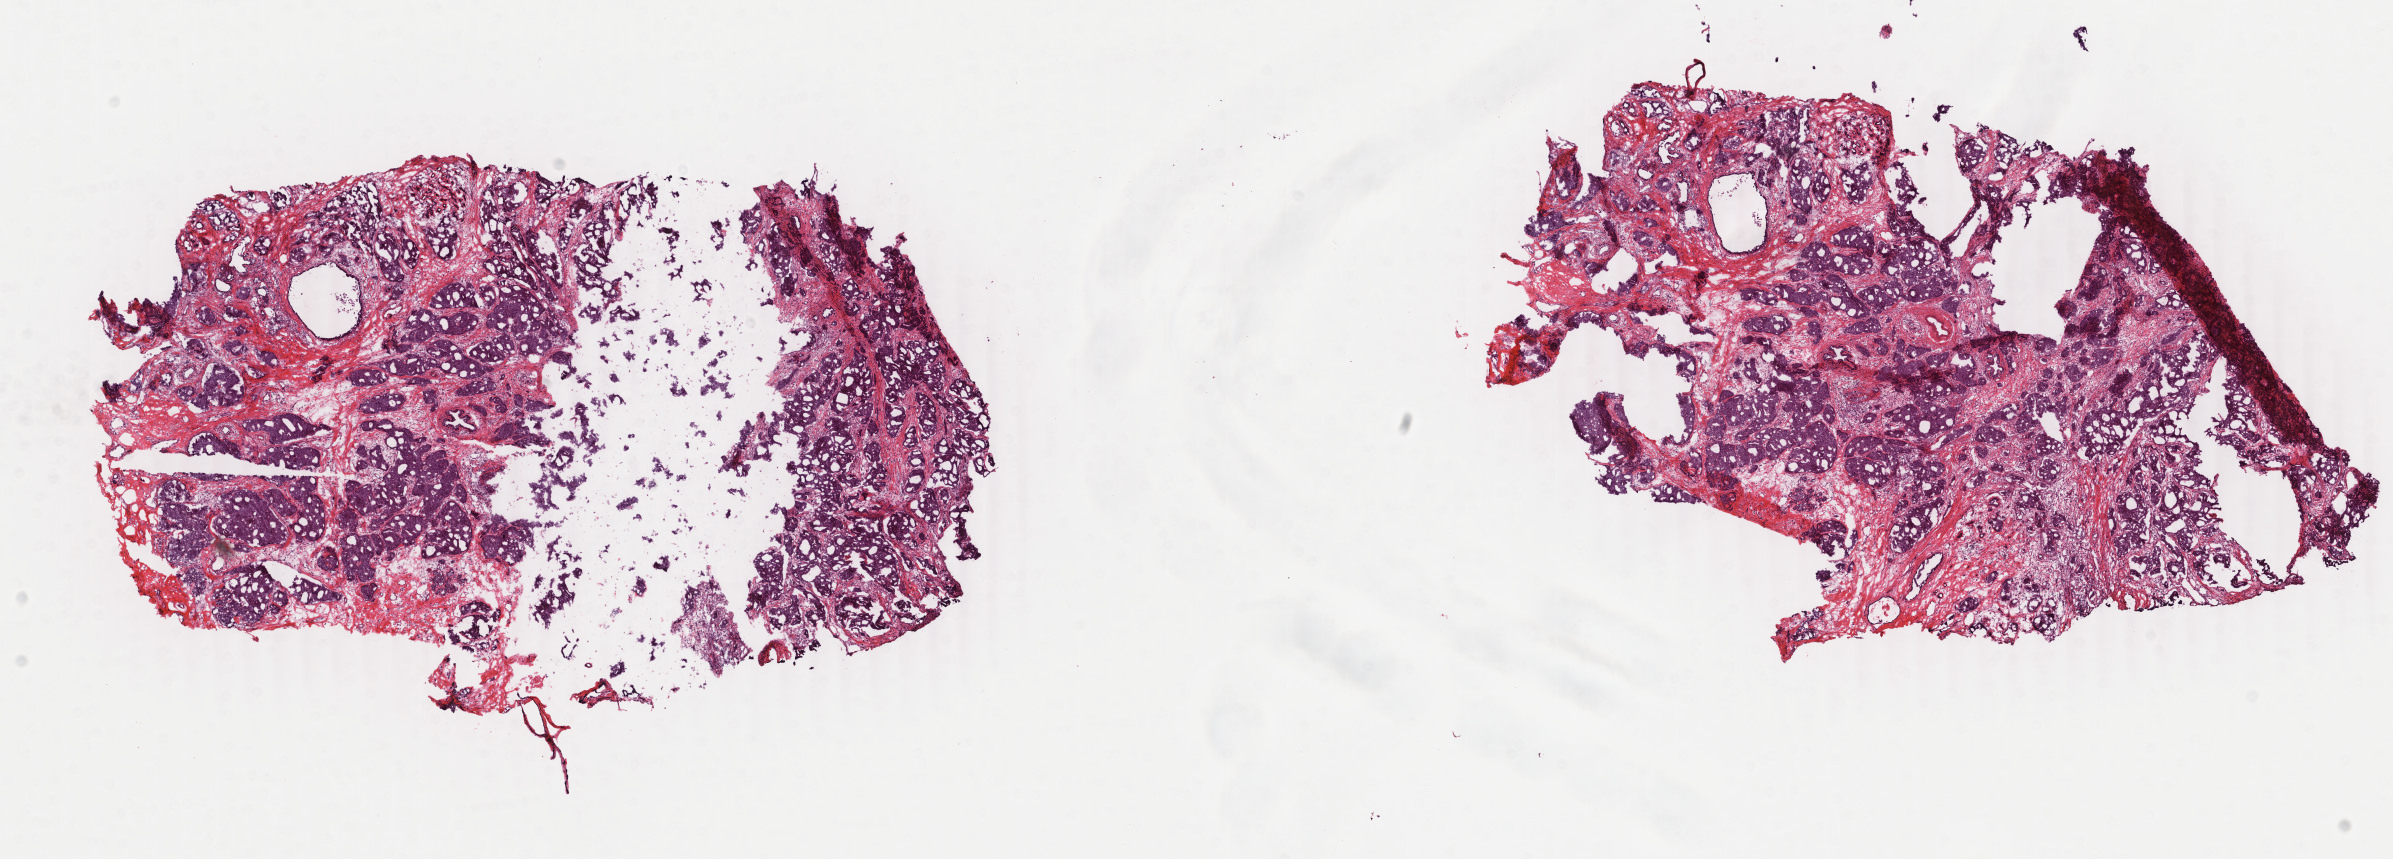
H&E-stained whole-slide image, shown as a low-resolution overview of the whole scanned area (about 19.0 x 6.8 mm); frozen section from the bottom of the tissue portion; sample: primary tumour, breast. Patient: female, age at initial diagnosis 54 years. Slide review estimates, as recorded: tumour cells 60%, tumour nuclei 60%.
Diagnosis: Cribriform carcinoma, NOS.